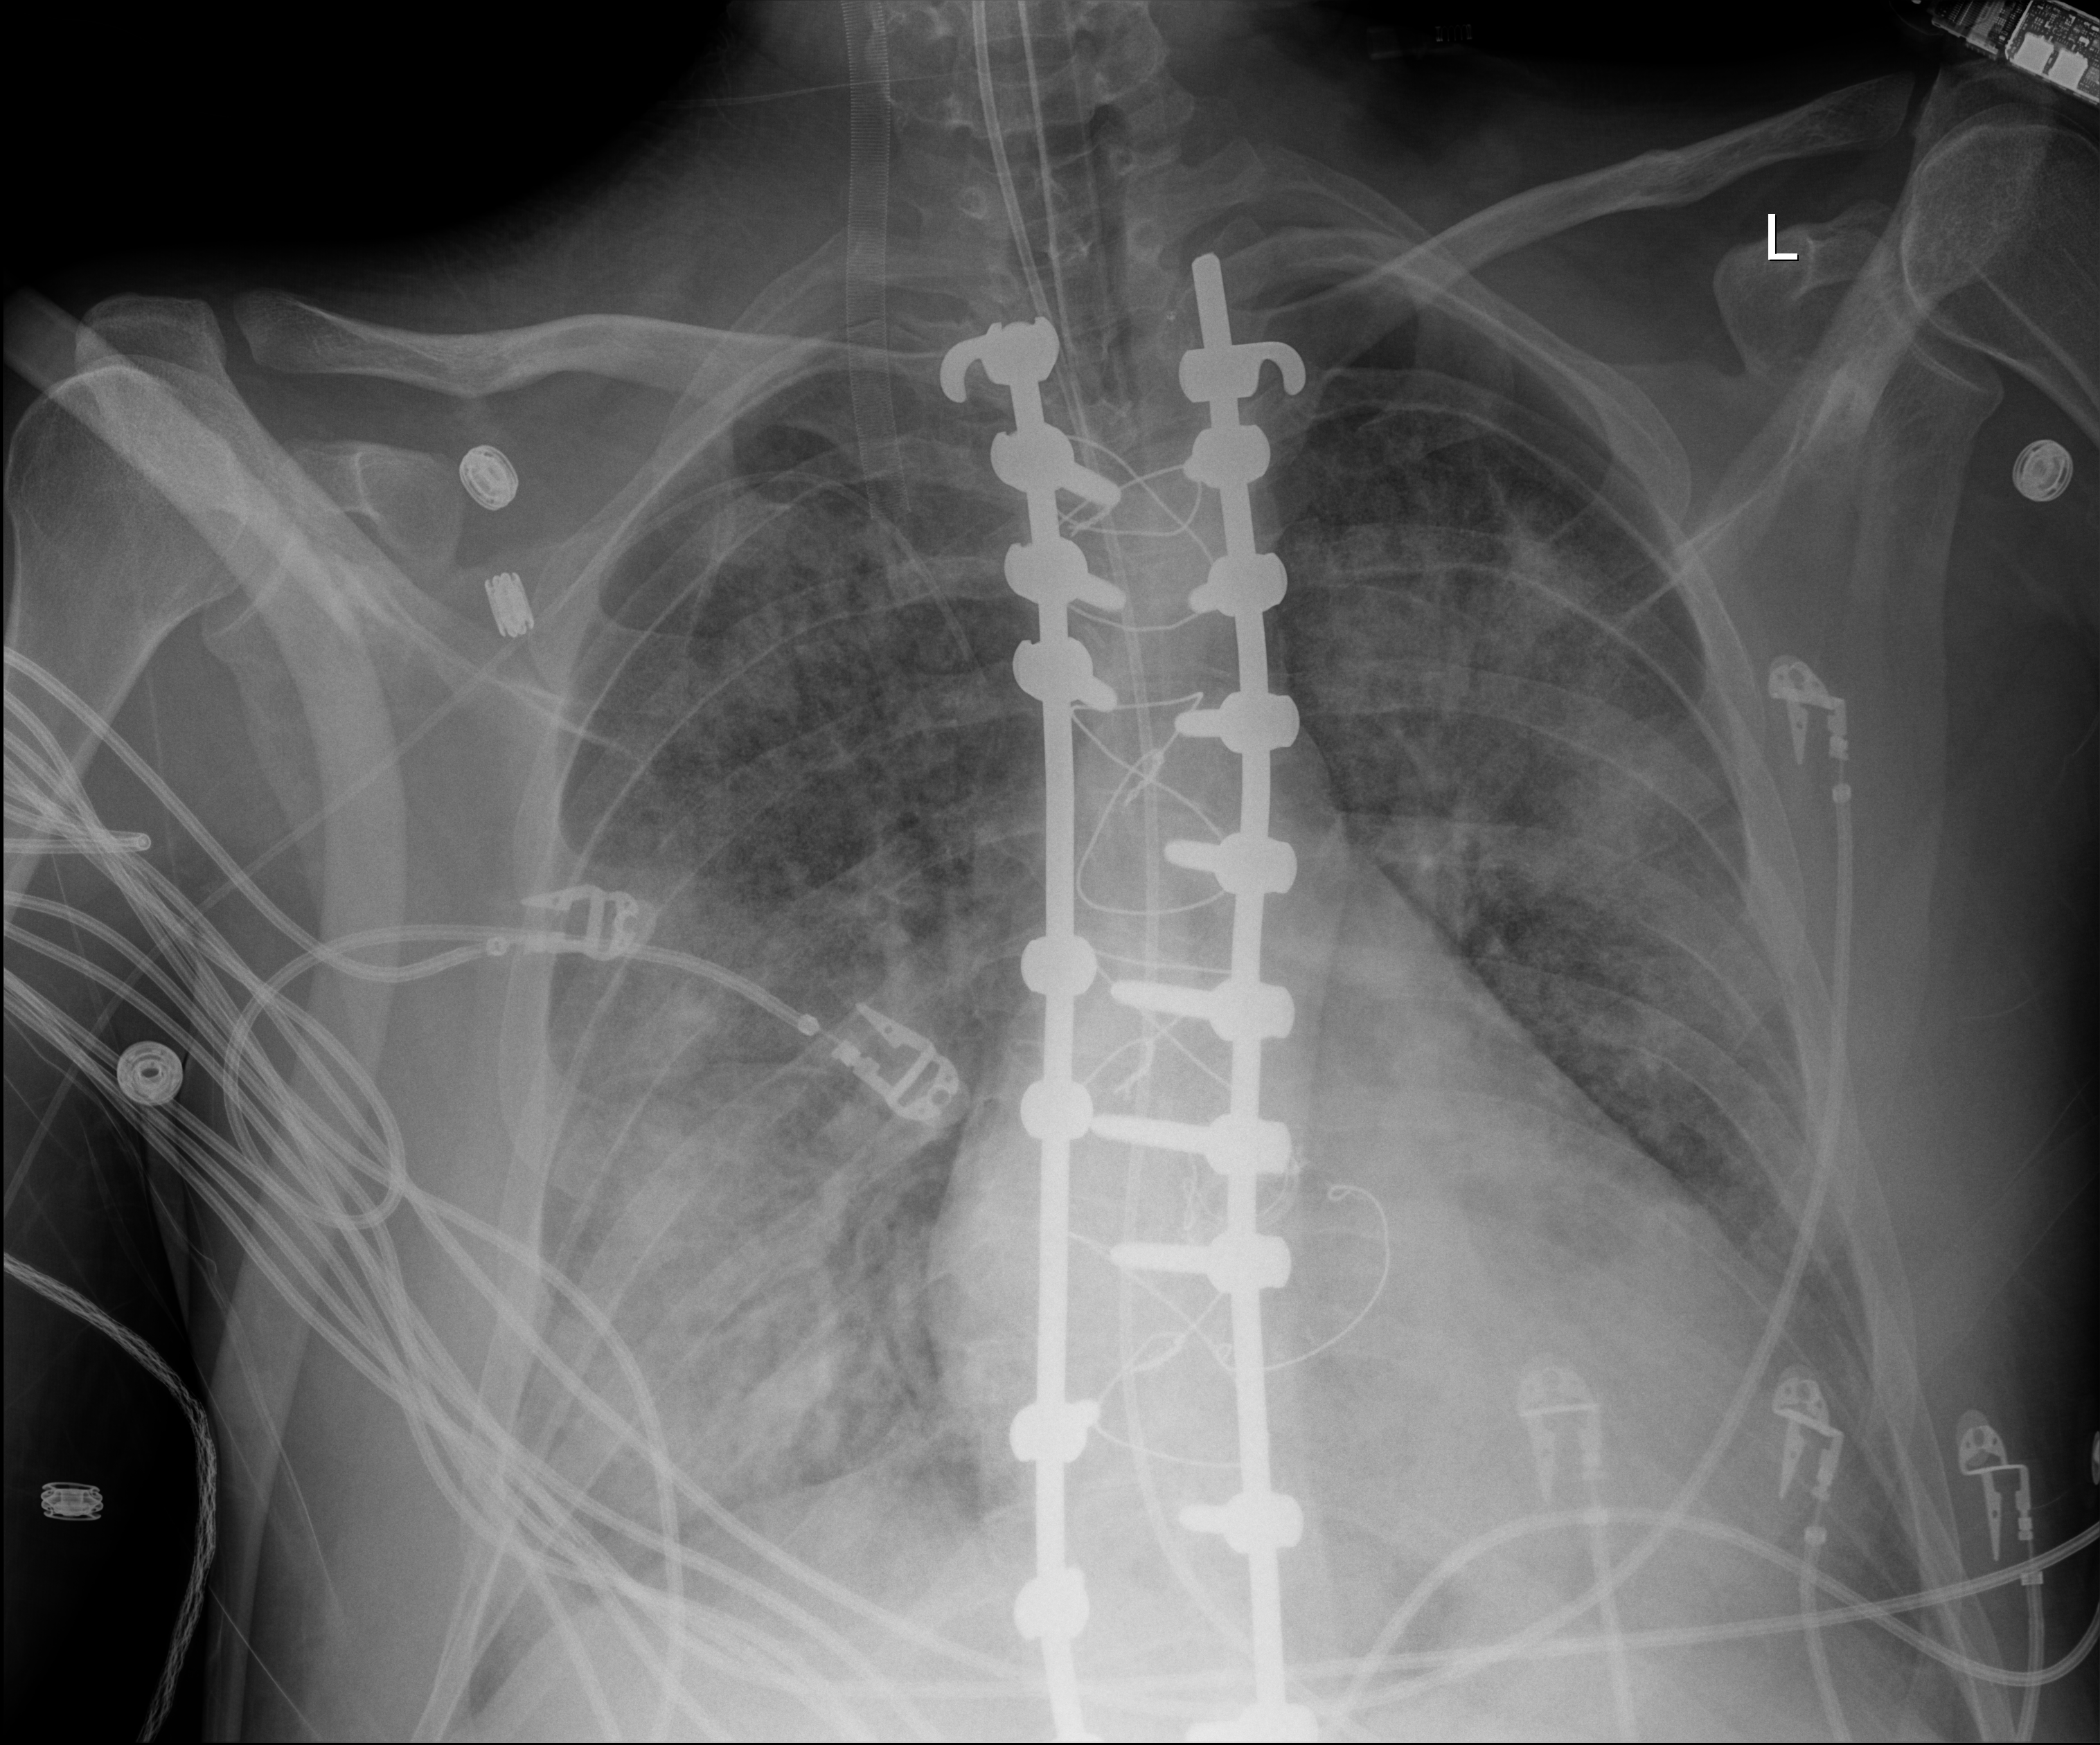
Portable chest radiograph. Adult patient hospitalised with COVID-19, age 18–59 years.
Admission-level facts for this patient (not findings on this image; timing relative to this image not recorded): COPD (admission record): no; mechanically ventilated during this hospital stay: yes; chronic kidney disease (admission record): no.